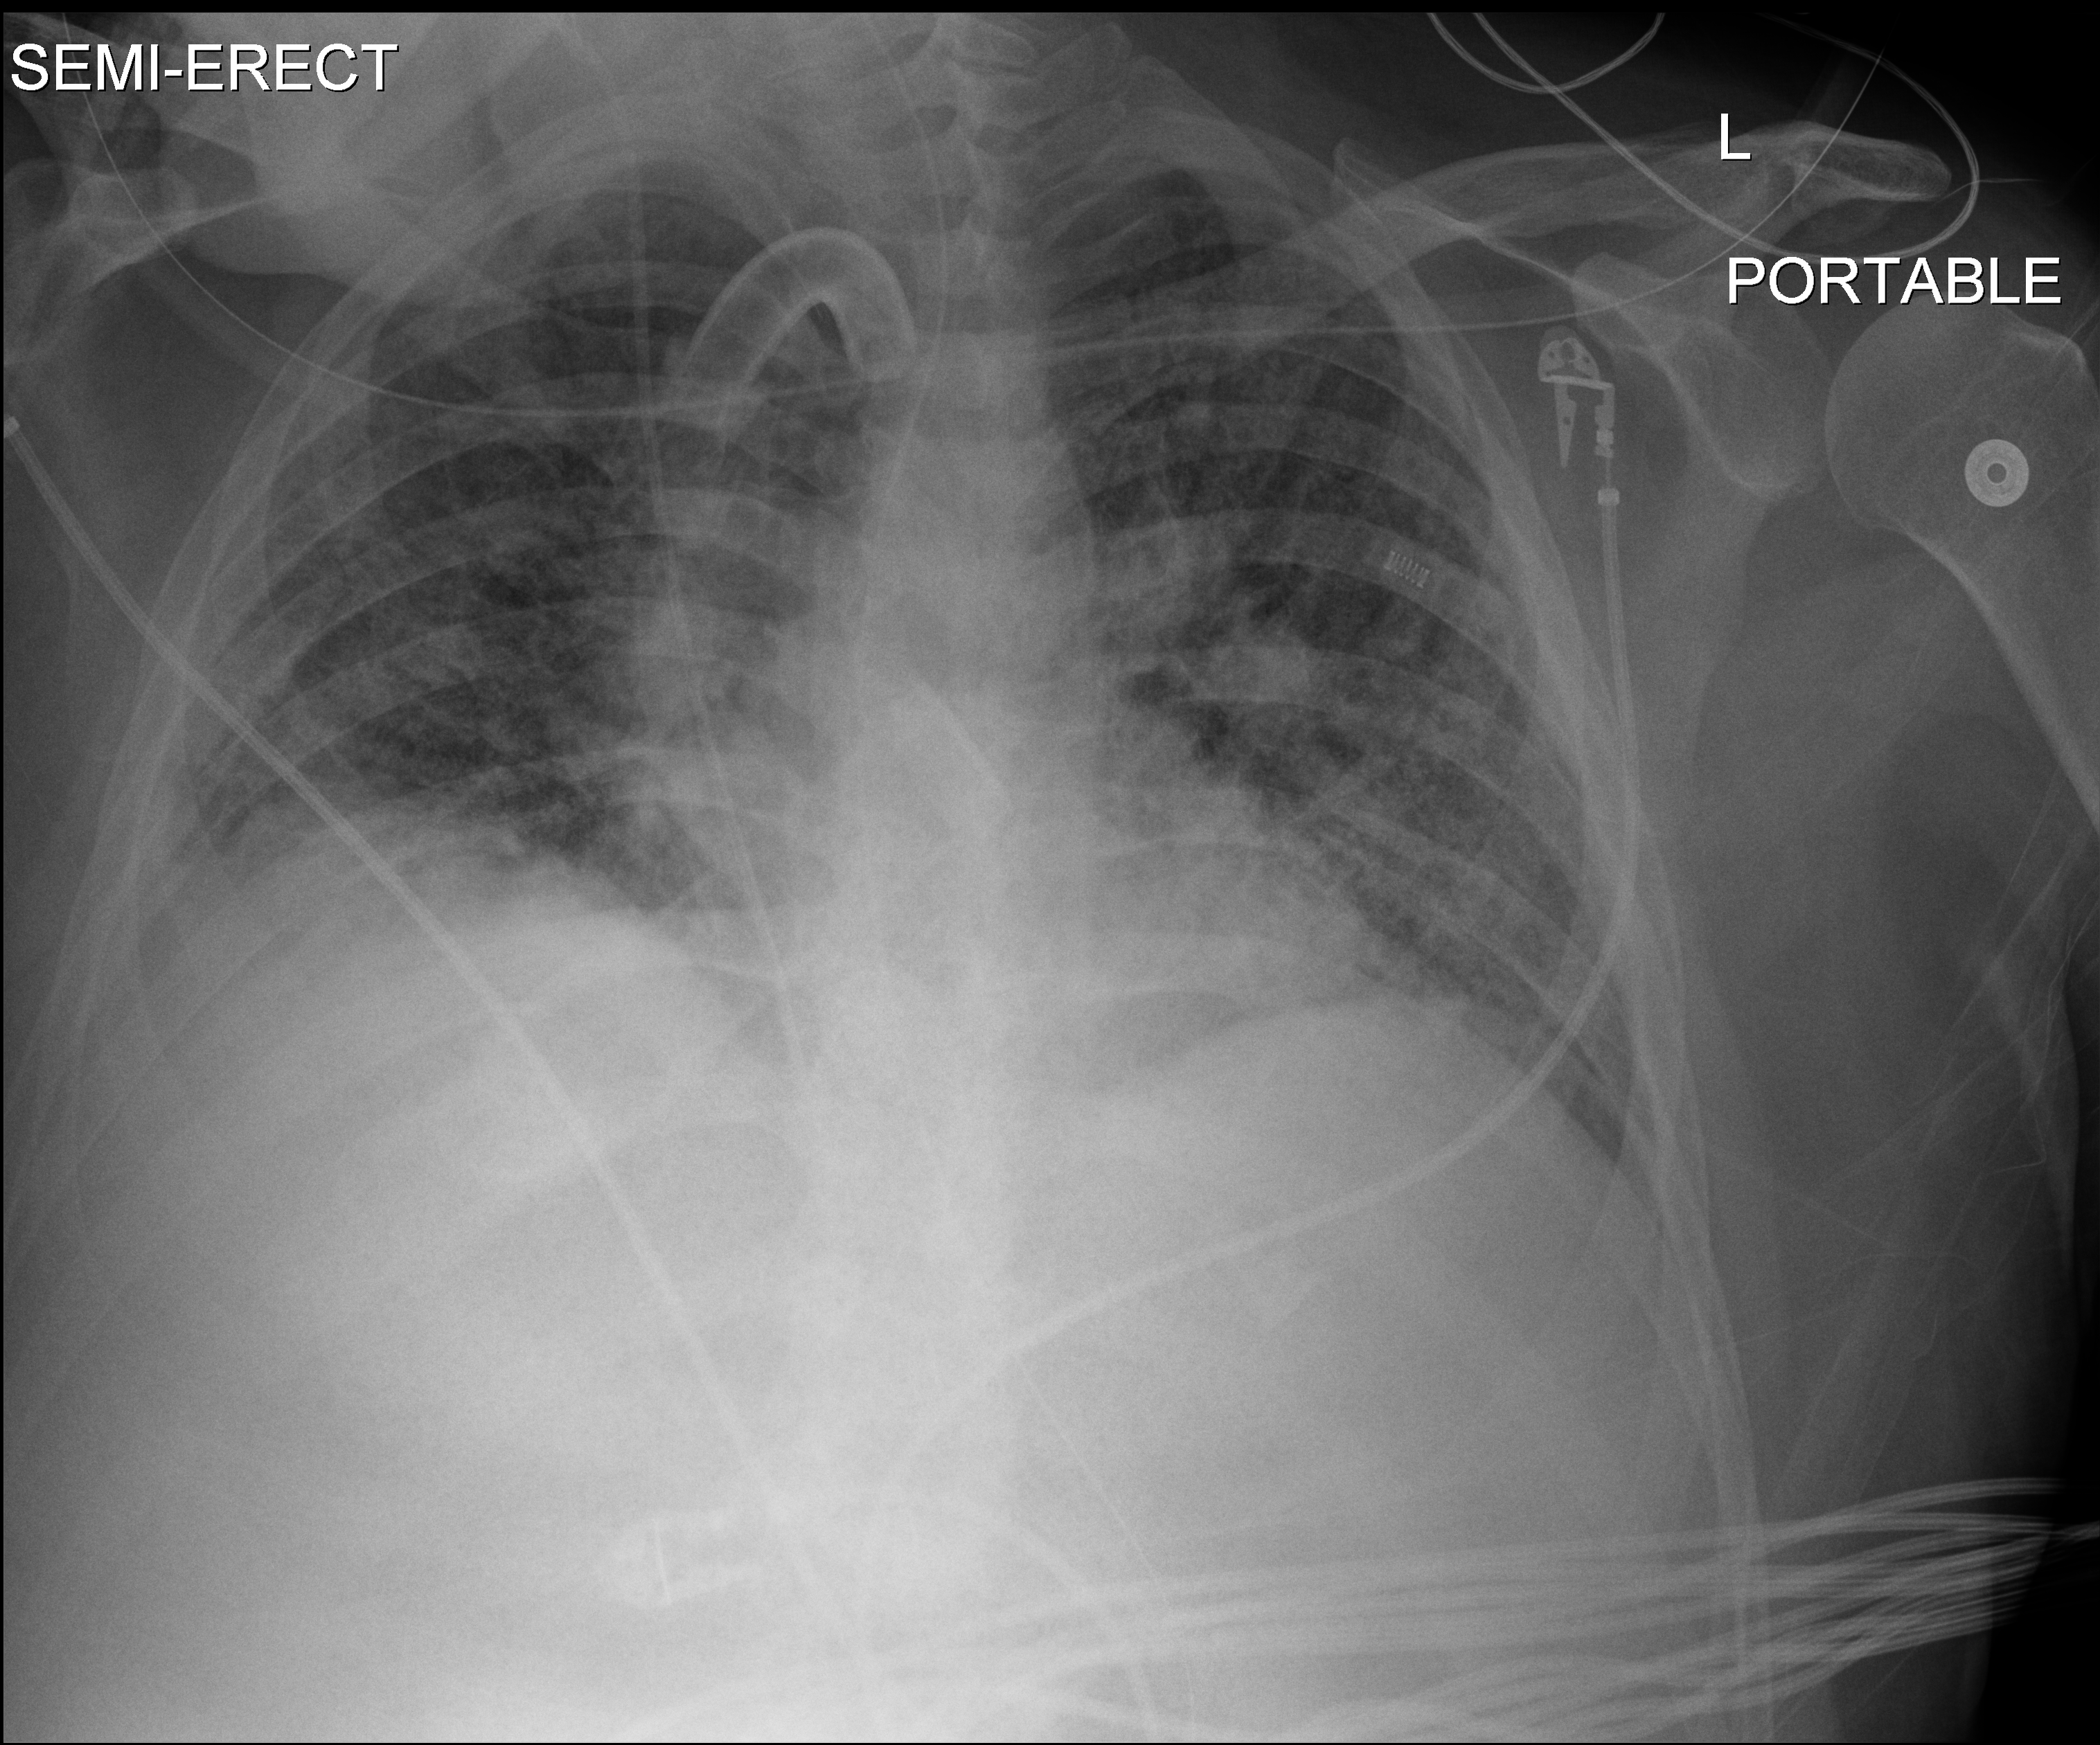
Chest X-ray, anteroposterior (AP) projection. Patient hospitalised with COVID-19; male, aged 18–59 years.
Admission-level facts for this patient (not findings on this image; timing relative to this image not recorded):
- admitted to intensive care during this hospital stay: yes
- COPD (admission record): no
- chronic kidney disease (admission record): no